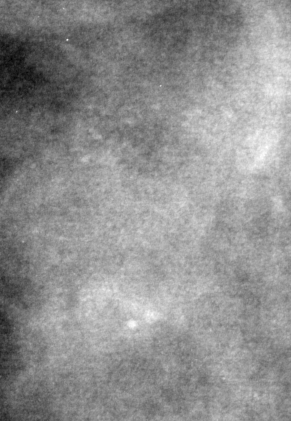
Crop from a digitized film mammogram around one marked abnormality, left breast, MLO view, BI-RADS breast density category 4 (scale 1–4).
Calcifications, morphology pleomorphic, distribution clustered; BI-RADS assessment category 4; pathology (as recorded): malignant.